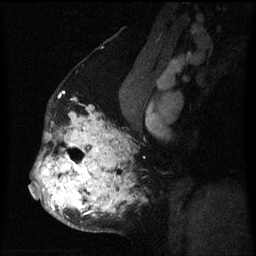
Breast MRI (dynamic contrast-enhanced), one sagittal slice; slice 36 of 60 in the series (ordered by position); dynamic contrast-enhanced series, image 2 of 3 at this slice position (ordered by acquisition); 1.5 T; TE 4.2 ms, TR 8 ms; 2 mm slice thickness; 256 × 256 image matrix, field of view 190 × 190 mm. Patient: female, 50 years.
Annotated regions visible in this slice (semi-automatically segmented with operator editing):
- analysis volume of interest (the breast-tissue region the enhancement analysis was run in; not a lesion): box from (x=32, y=98) to (x=136, y=232) px
- tumour enhancement mask (voxels above the 70 % enhancement threshold inside the analysis volume of interest): (x=32, y=99)–(x=130, y=216)